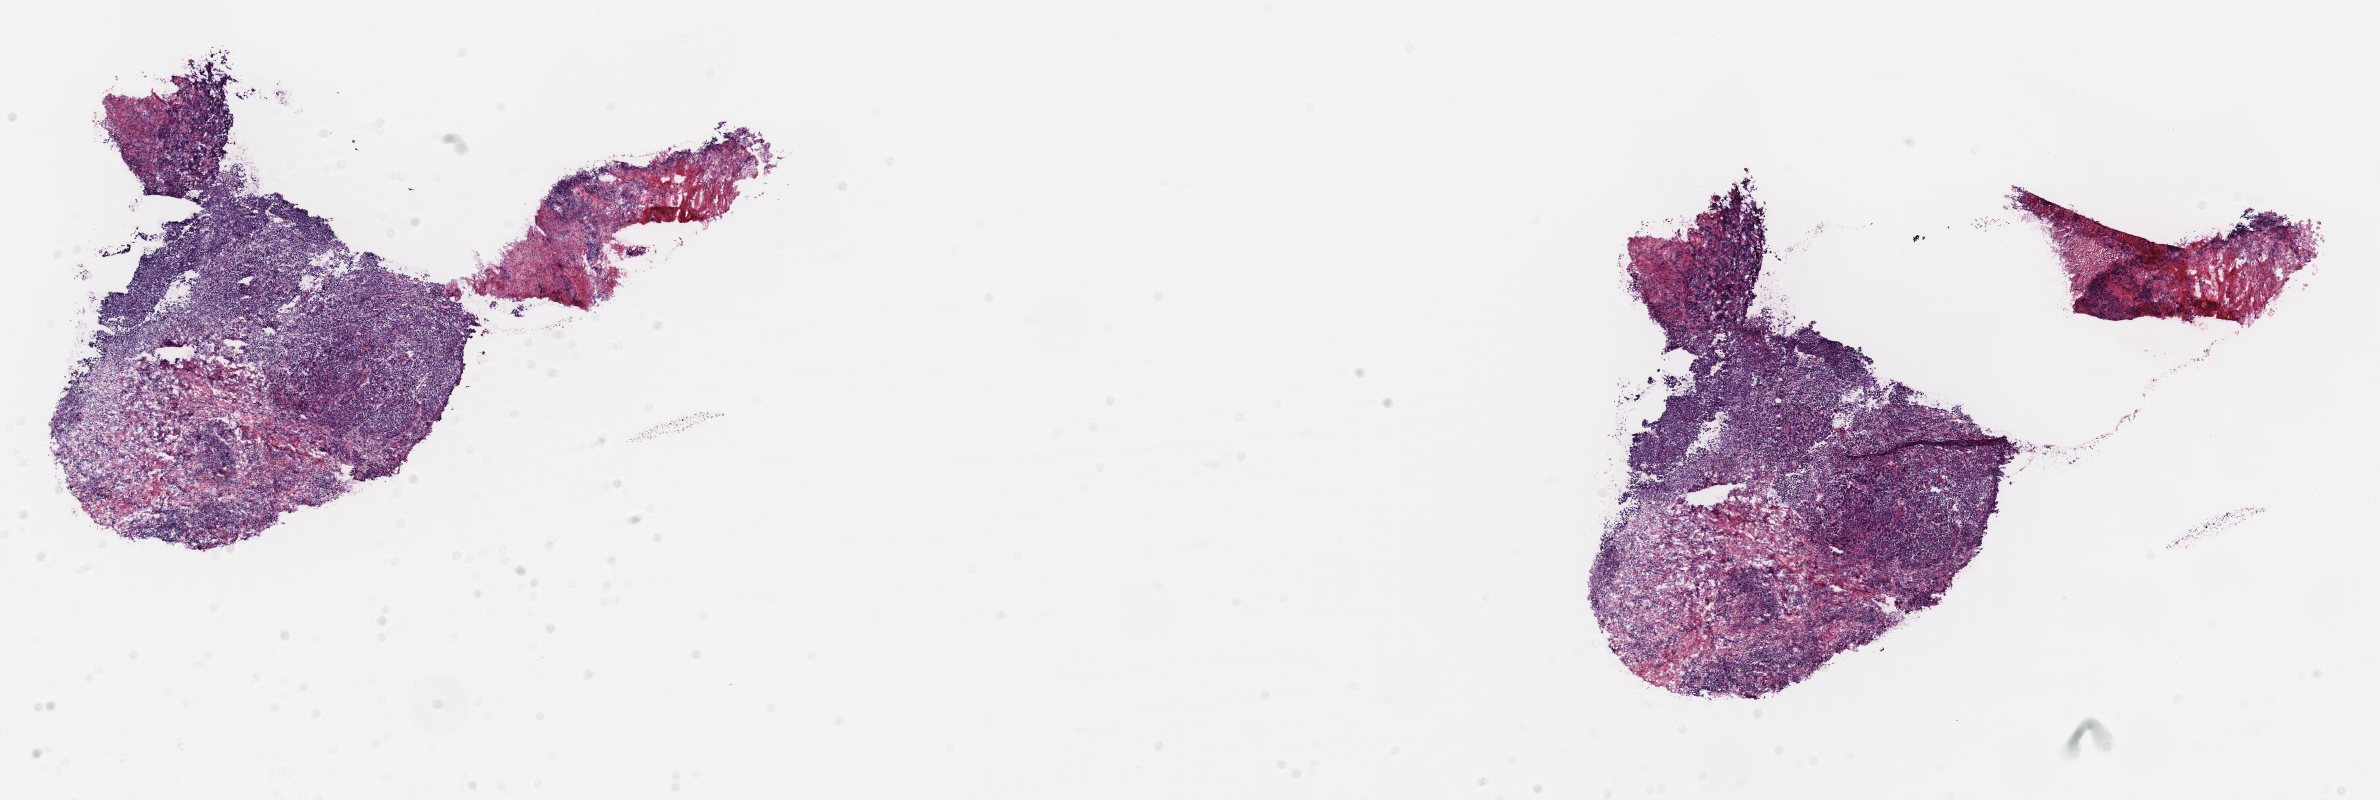
Whole-slide histology image, H&E, low-resolution overview of the scanned area, about 18.8 x 6.3 mm (slide scanned at 40x); frozen section; cervix, primary tumour sample. Patient: female, age at initial diagnosis 88 years. Histologic grade: G3 (poorly differentiated). Pathologist review of this section (percent, as recorded): tumour cells 50%, tumour nuclei 60%, normal cells 29%, stromal cells 20%, necrosis 1%. Infiltration values recorded for this section: lymphocyte infiltration 15%, monocyte infiltration 0%, neutrophil infiltration 0%.
• diagnosis: Squamous cell carcinoma, NOS (cervix uteri)